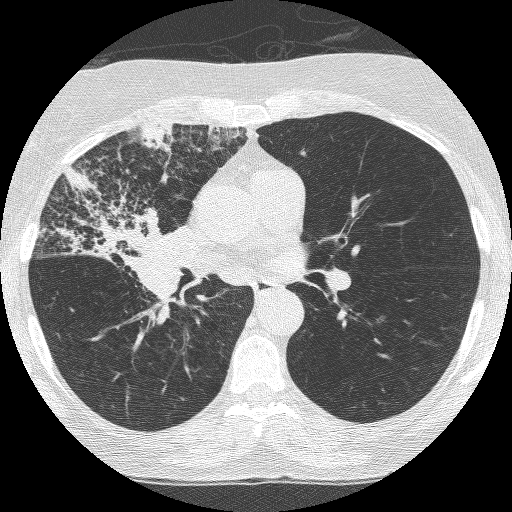
Axial slice from a low-dose chest CT screening exam; third screening round (two years after baseline); lung window (W 1500 / L -600 HU); lung (sharp) reconstruction kernel (BONE). Female, age 64 years at enrolment. Former smoker at enrolment.
- Expert-annotated lung lesion, bounding box (x1, y1, x2, y2) in pixels: (64, 176, 201, 315).
- The exam's reader record, not a measurement of the box and not confirmed to be the same lesion: non-calcified nodule or mass ≥4 mm, right upper lobe, 49 × 43 mm, spiculated (stellate) margins, soft tissue attenuation, pre-existing on the prior screen: yes; interval growth: yes.
- Official screen result: positive, other.
- Participant outcome: lung cancer diagnosed 7 days after this screen — adenocarcinoma, NOS, right upper lobe, right middle lobe, right hilum, stage IV (AJCC 6th edition), 85 mm at pathology.